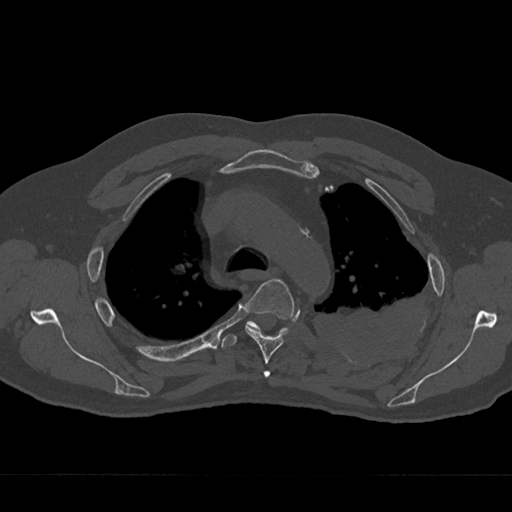
CT including the spine, one axial slice; position 511 of 797 along the scan axis; bone window (W 1800 / L 400 HU); 0.5 mm slice thickness; 512 × 512 image matrix, field of view 377 × 377 mm. Male patient, age 75 years. From the clinical record (not read from this slice): primary cancer: renal; vertebrae with lytic lesions (as recorded): T4.
Annotated regions visible in this slice (semi-automatic segmentation, software-assisted and operator-edited):
- T3 vertebra: bounding box <263,371,270,377> (left, top, right, bottom; pixels)
- T4 vertebra: <245,279,294,376>
- T5 vertebra: <221,320,286,349>